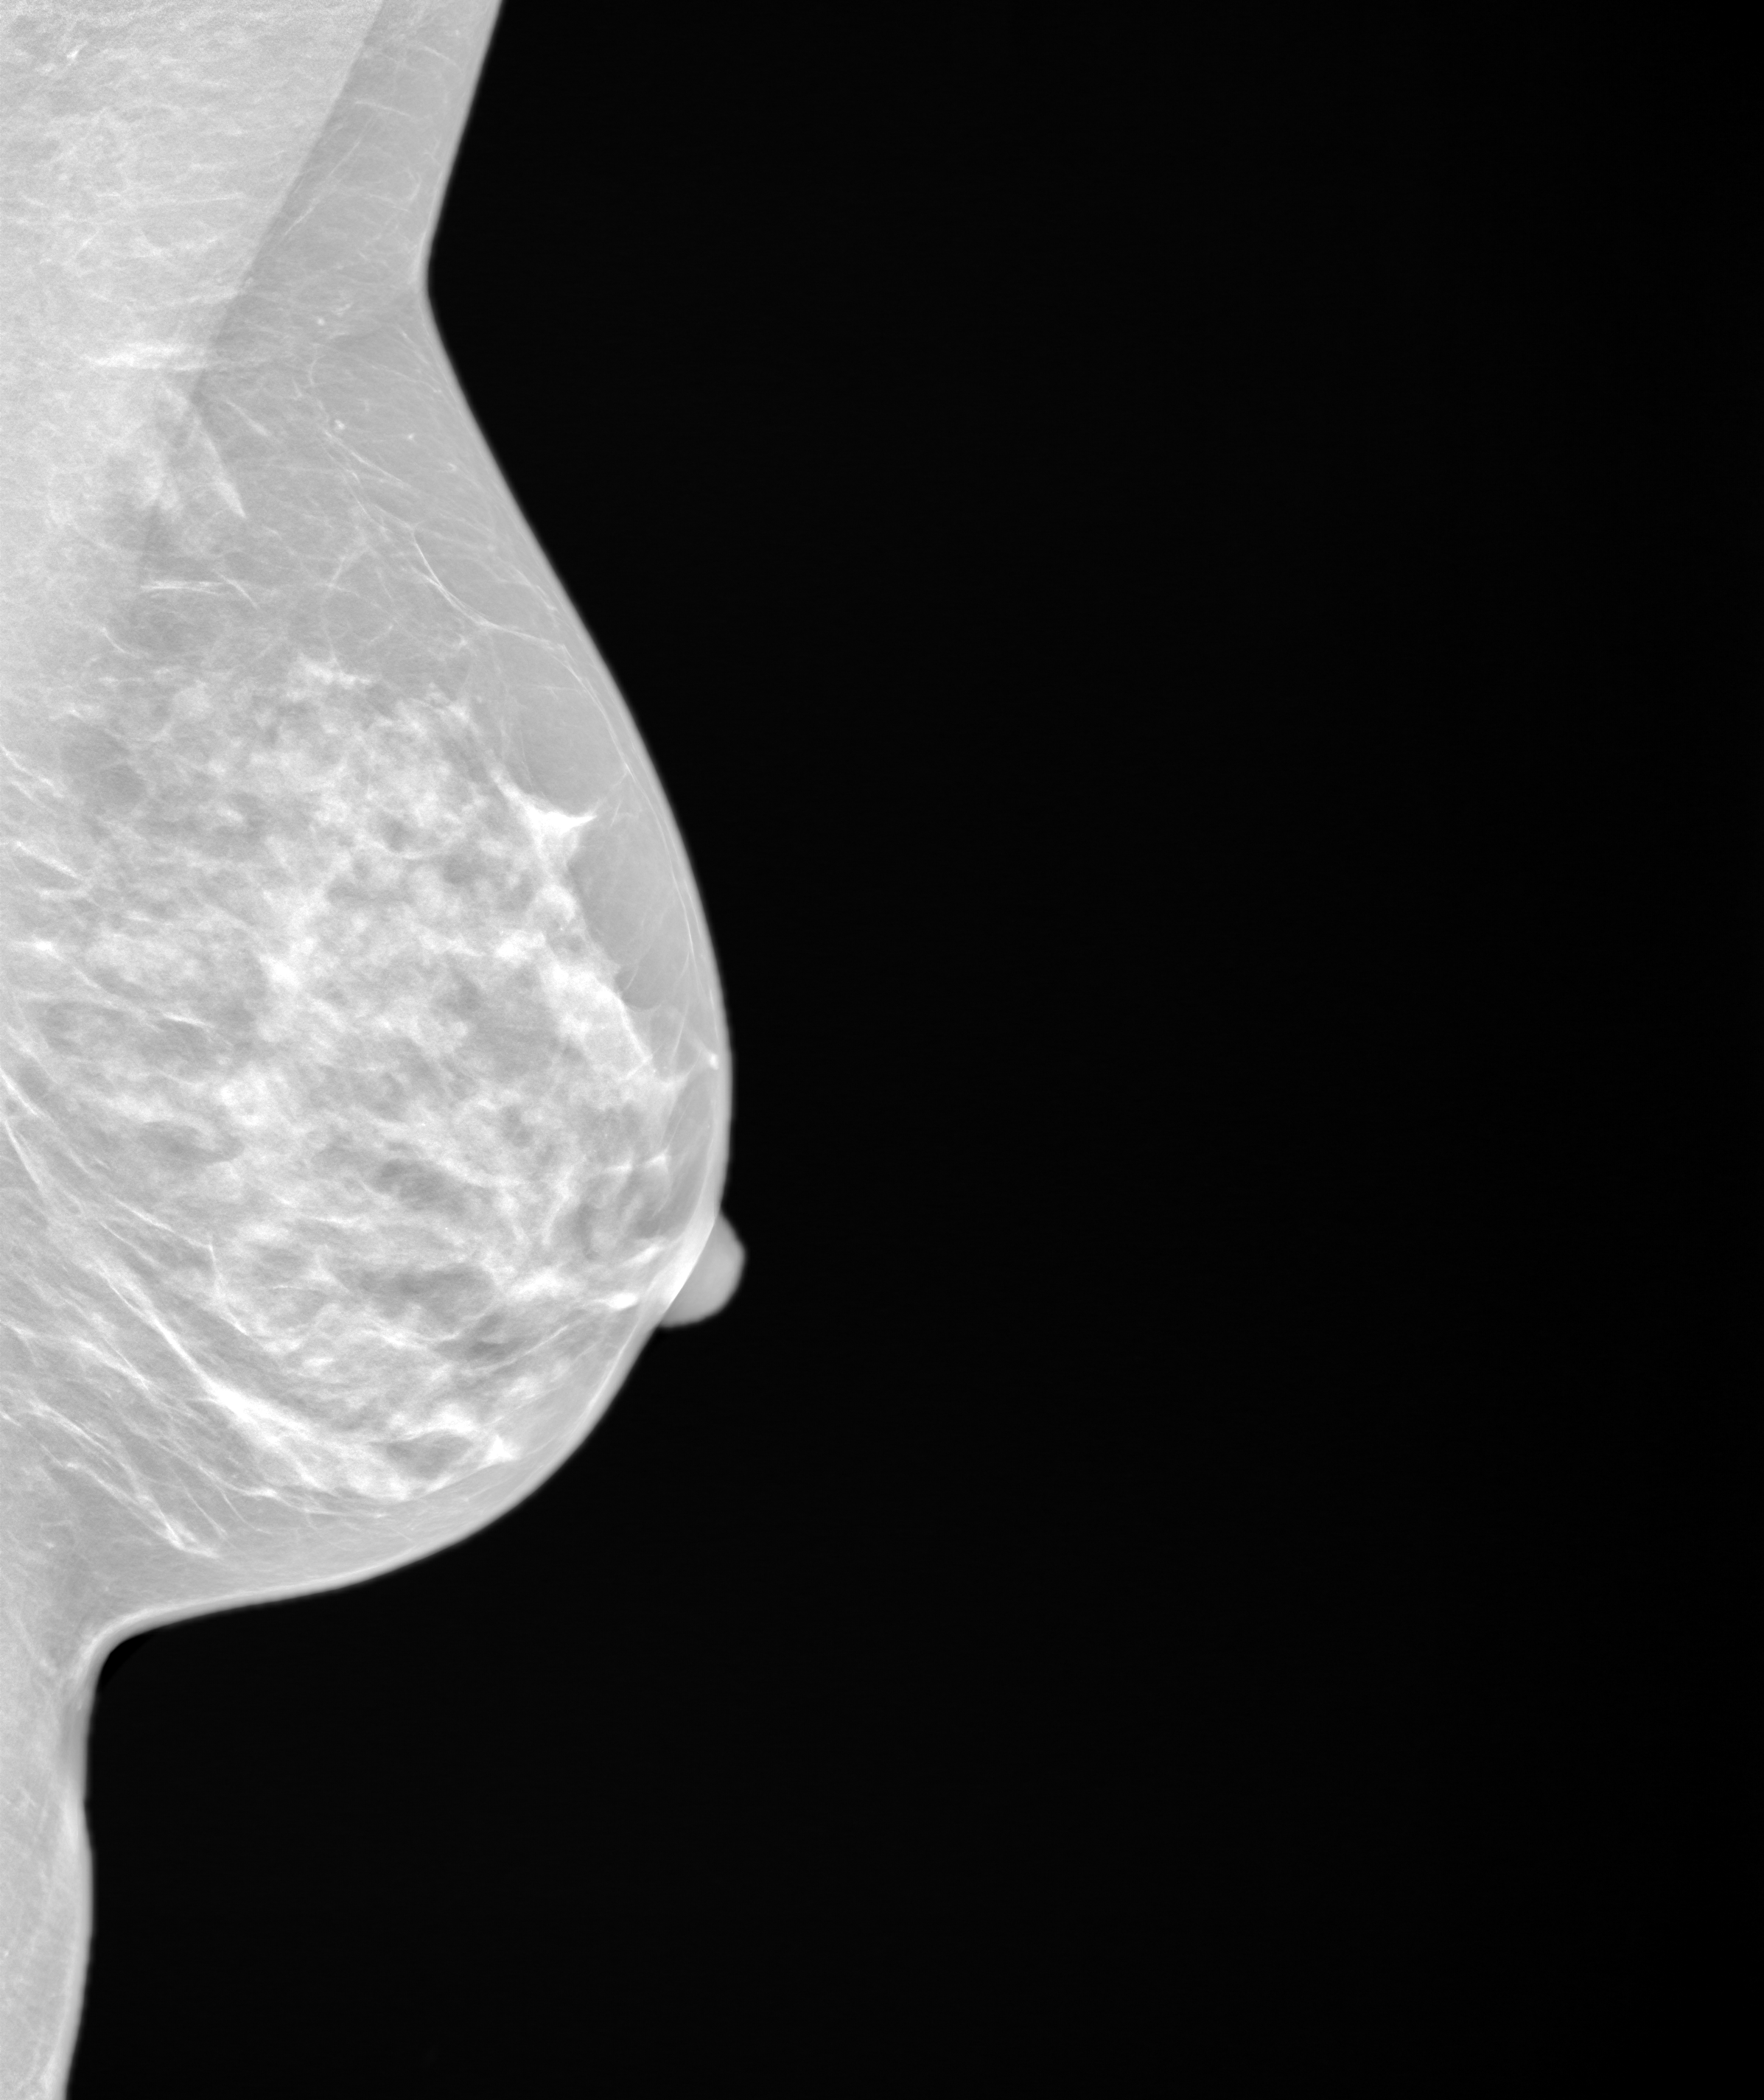
Annual screening mammography examination, system: SenoIris_1SP2(440). Patient: female, 59 years.
Image type: synthesized 2-D view from tomosynthesis. Breast: left. Projection: MLO view.